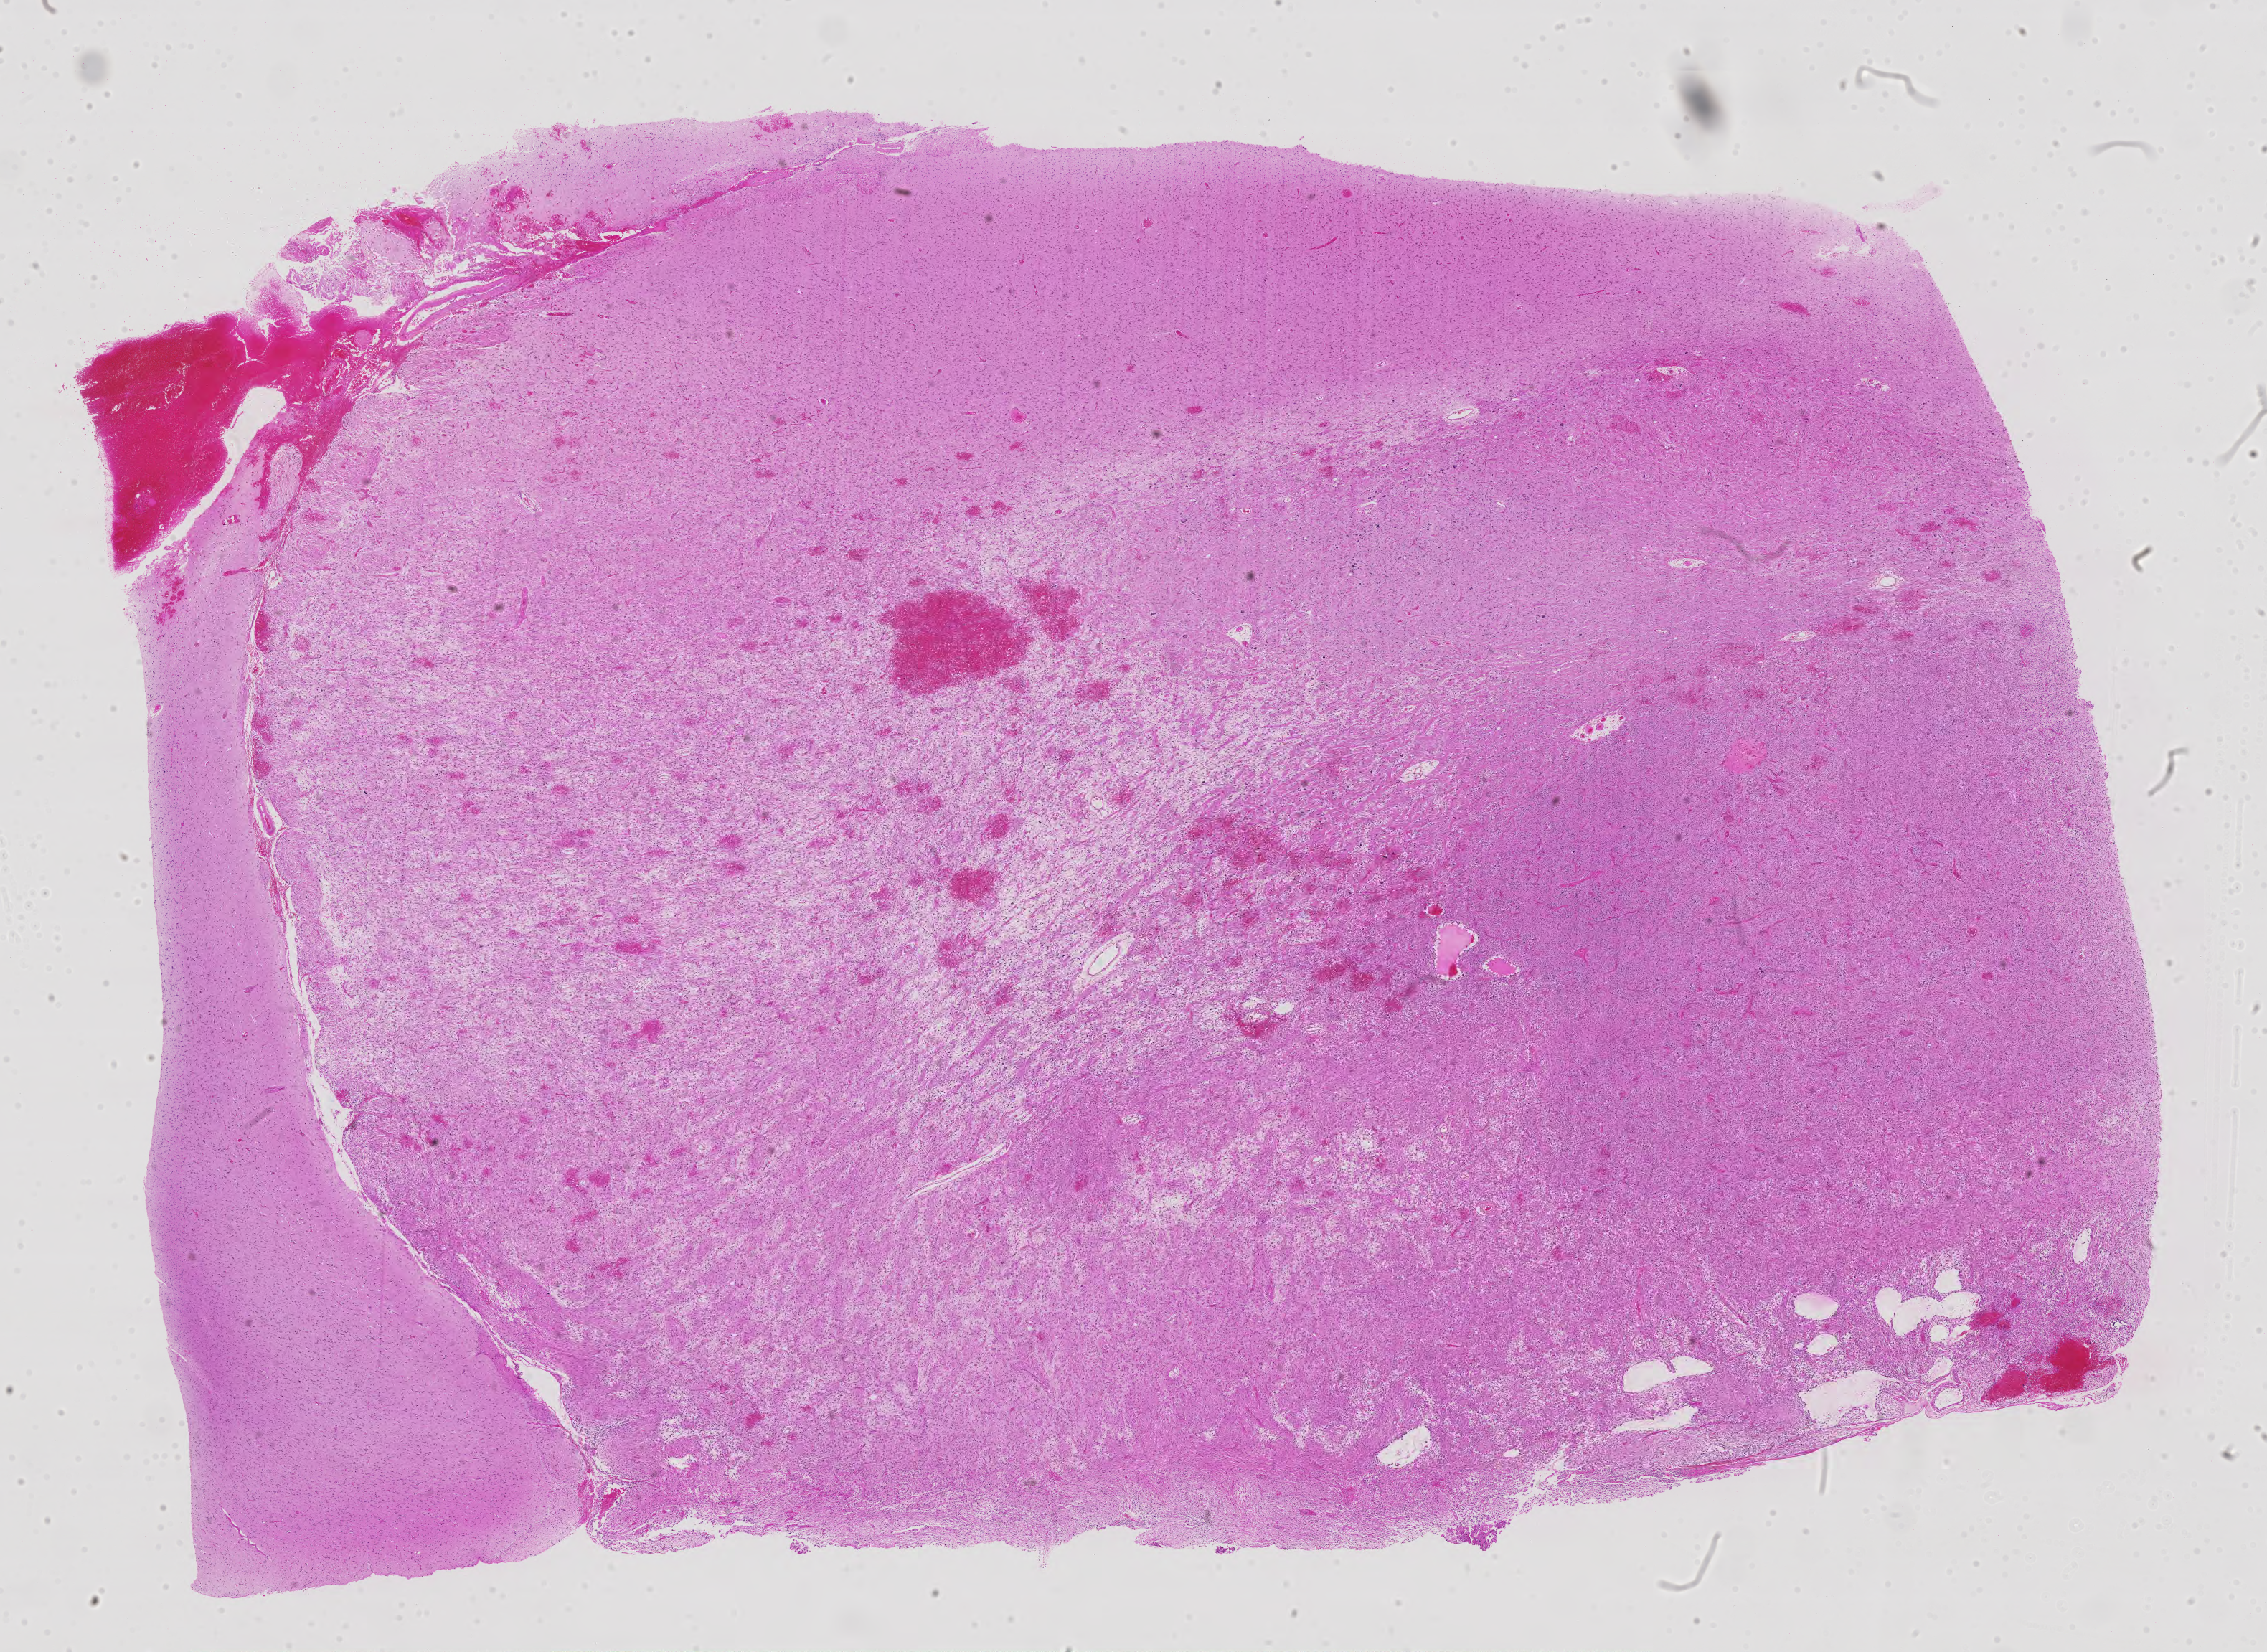
Digitized H&E tissue section (whole slide), low-resolution overview of the scanned area, about 25.3 x 18.4 mm (acquisition: 40x scan); formalin-fixed paraffin-embedded (FFPE) diagnostic section; brain, primary tumour sample. Female, age 32 years at initial diagnosis. Histologic grade: G3 (poorly differentiated).
Histologic diagnosis: Astrocytoma, anaplastic. Laterality: left.